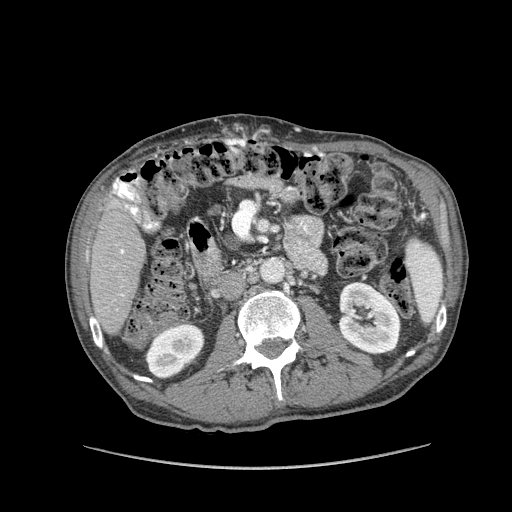
Contrast-enhanced abdominal CT (liver protocol), one axial slice. Position 27 of 162 along the scan axis. Reconstruction kernel STANDARD. 100 kVp. Soft-tissue window (W 400 / L 40 HU). 2.5 mm slice thickness. 512 × 512 image matrix, field of view 400 × 400 mm. From the clinical record (not read from this slice): diagnosis: hepatocellular carcinoma (patient treated with transarterial chemoembolisation; whether this scan precedes or follows treatment is not stated here); TNM stage (as recorded): Stage-IIIA; Child-Pugh class: A; tumour nodularity: multinodular; tumour size: 9.9 cm.
Structures marked on this image (semi-automatic segmentation, software-assisted and operator-edited):
- liver parenchyma outside the tumour (the mass and vessels are separate outlines, so this box may not span the whole liver): bounding box (x1, y1, x2, y2) in pixels: (90, 196, 146, 334)
- liver vessels: (120, 249, 124, 296)